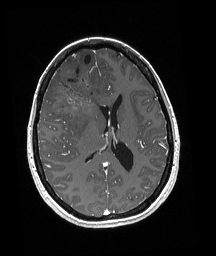
Brain MRI from a brain-tumour surgery series, one axial slice. Slice 86 of 192 in the series (ordered by position). T1-weighted post-contrast. 1 mm slice thickness. 216 × 256 image matrix, field of view 211 × 250 mm. Case-level facts recorded for this patient, not image findings: histopathology: Oligodendroglioma; WHO grade: 3; IDH mutation: yes; tumour location: Right Frontal.
Structures marked on this image (expert manual segmentation):
- tumour: bounding box <53,76,101,116> (left, top, right, bottom; pixels)